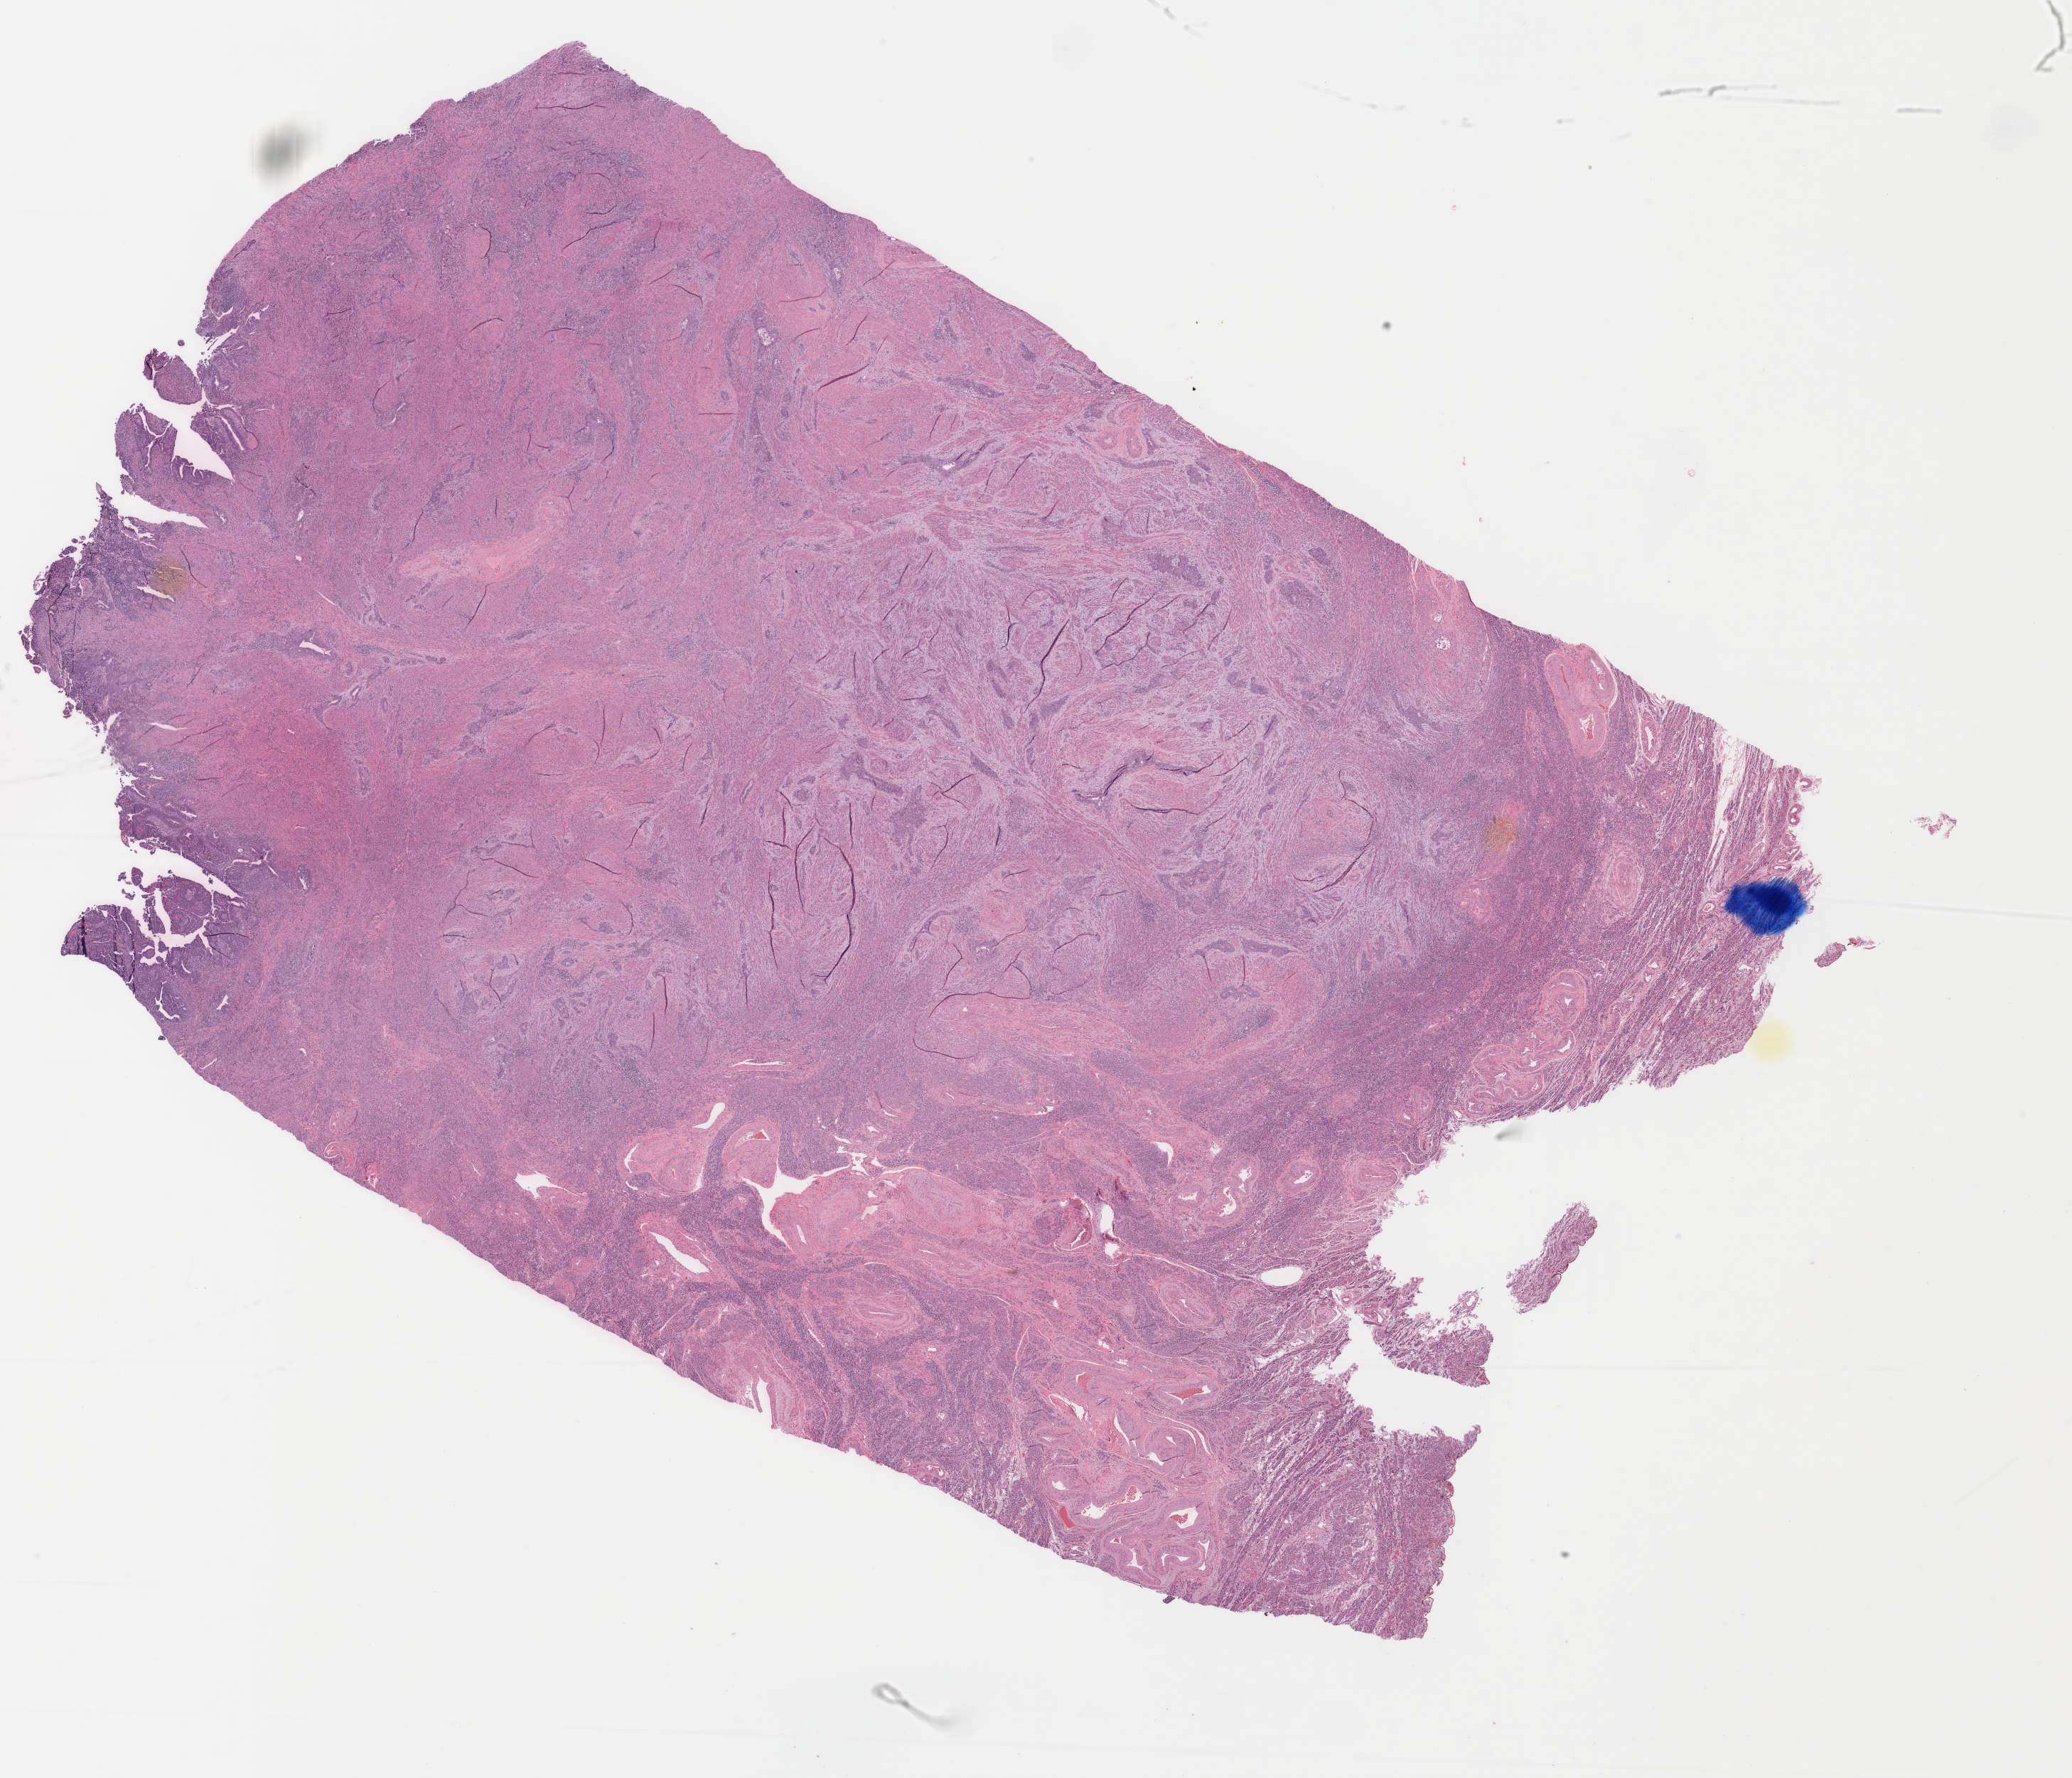
Whole-slide histology image, H&E-stained, a low-resolution overview of the entire scanned area, about 23.1 x 19.9 mm (acquisition: 40x scan). Formalin-fixed paraffin-embedded (FFPE) diagnostic section. Primary tumour sample from the uterus. Female, age 65 years at initial diagnosis. Histologic grade: G3 (poorly differentiated).
FIGO stage: IC. Lymph nodes positive (case pathology): 0 of 11 examined. Pathologic diagnosis: Serous cystadenocarcinoma, NOS.